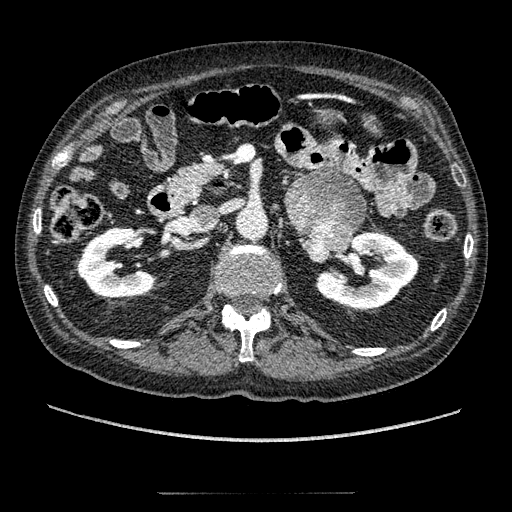
Contrast-enhanced abdominal CT, one axial slice; slice 101 of 274 in the series (ordered by position); reconstruction kernel STANDARD; intravenous contrast given; soft-tissue window (W 400 / L 40 HU); 512 × 512 image matrix, field of view 381 × 381 mm. Male patient, age 69 years. From the clinical record (not read from this slice): diagnosis: adrenocortical carcinoma; tumour side: left adrenal; tumour size at pathology: 6.1 cm; Ki-67 index: 10 %; stage (as recorded): 3.
Structures marked on this image (semi-automatic segmentation, software-assisted and operator-edited):
- mass: bounding box (x1, y1, x2, y2) in pixels: (286, 174, 364, 261)